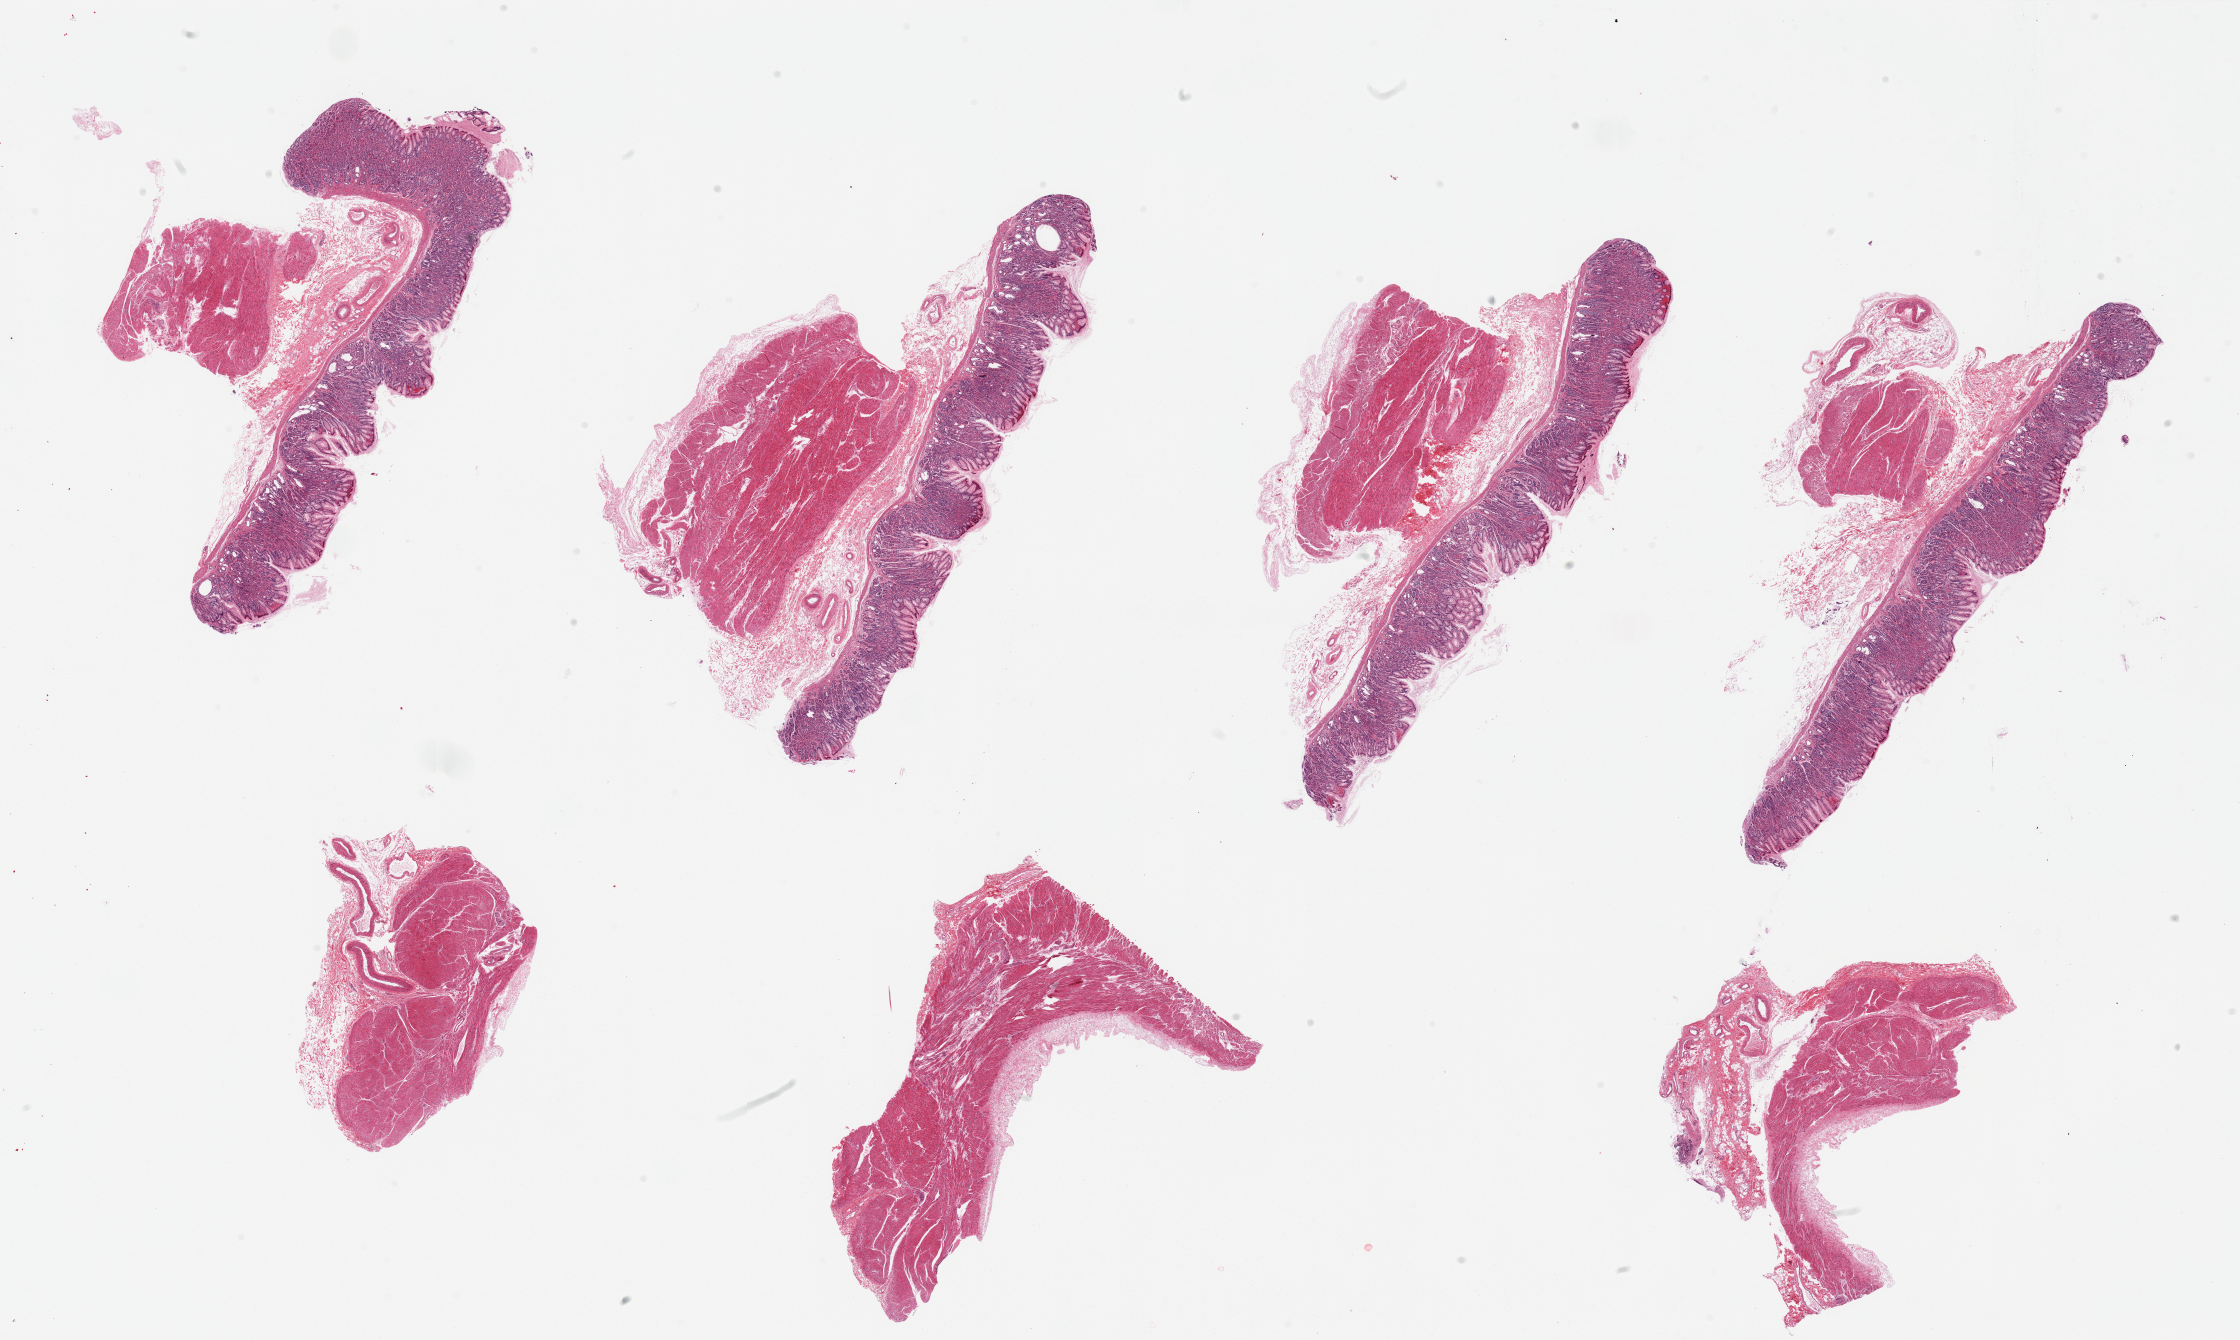
Whole-slide image, hematoxylin and eosin (H&E) stain, whole scanned area (about 35.4 x 21.2 mm, slide scanned at 20x) shown as a low-resolution overview; PAXgene-fixed, paraffin-embedded tissue; target tissue: stomach; tissue donor sample. Donor sex: male.
Reviewer comment on this tissue sample: 7 pieces, 4 pieces with mucosa and muscularis, 3 essentially muscle only (minute focus of mucosa).